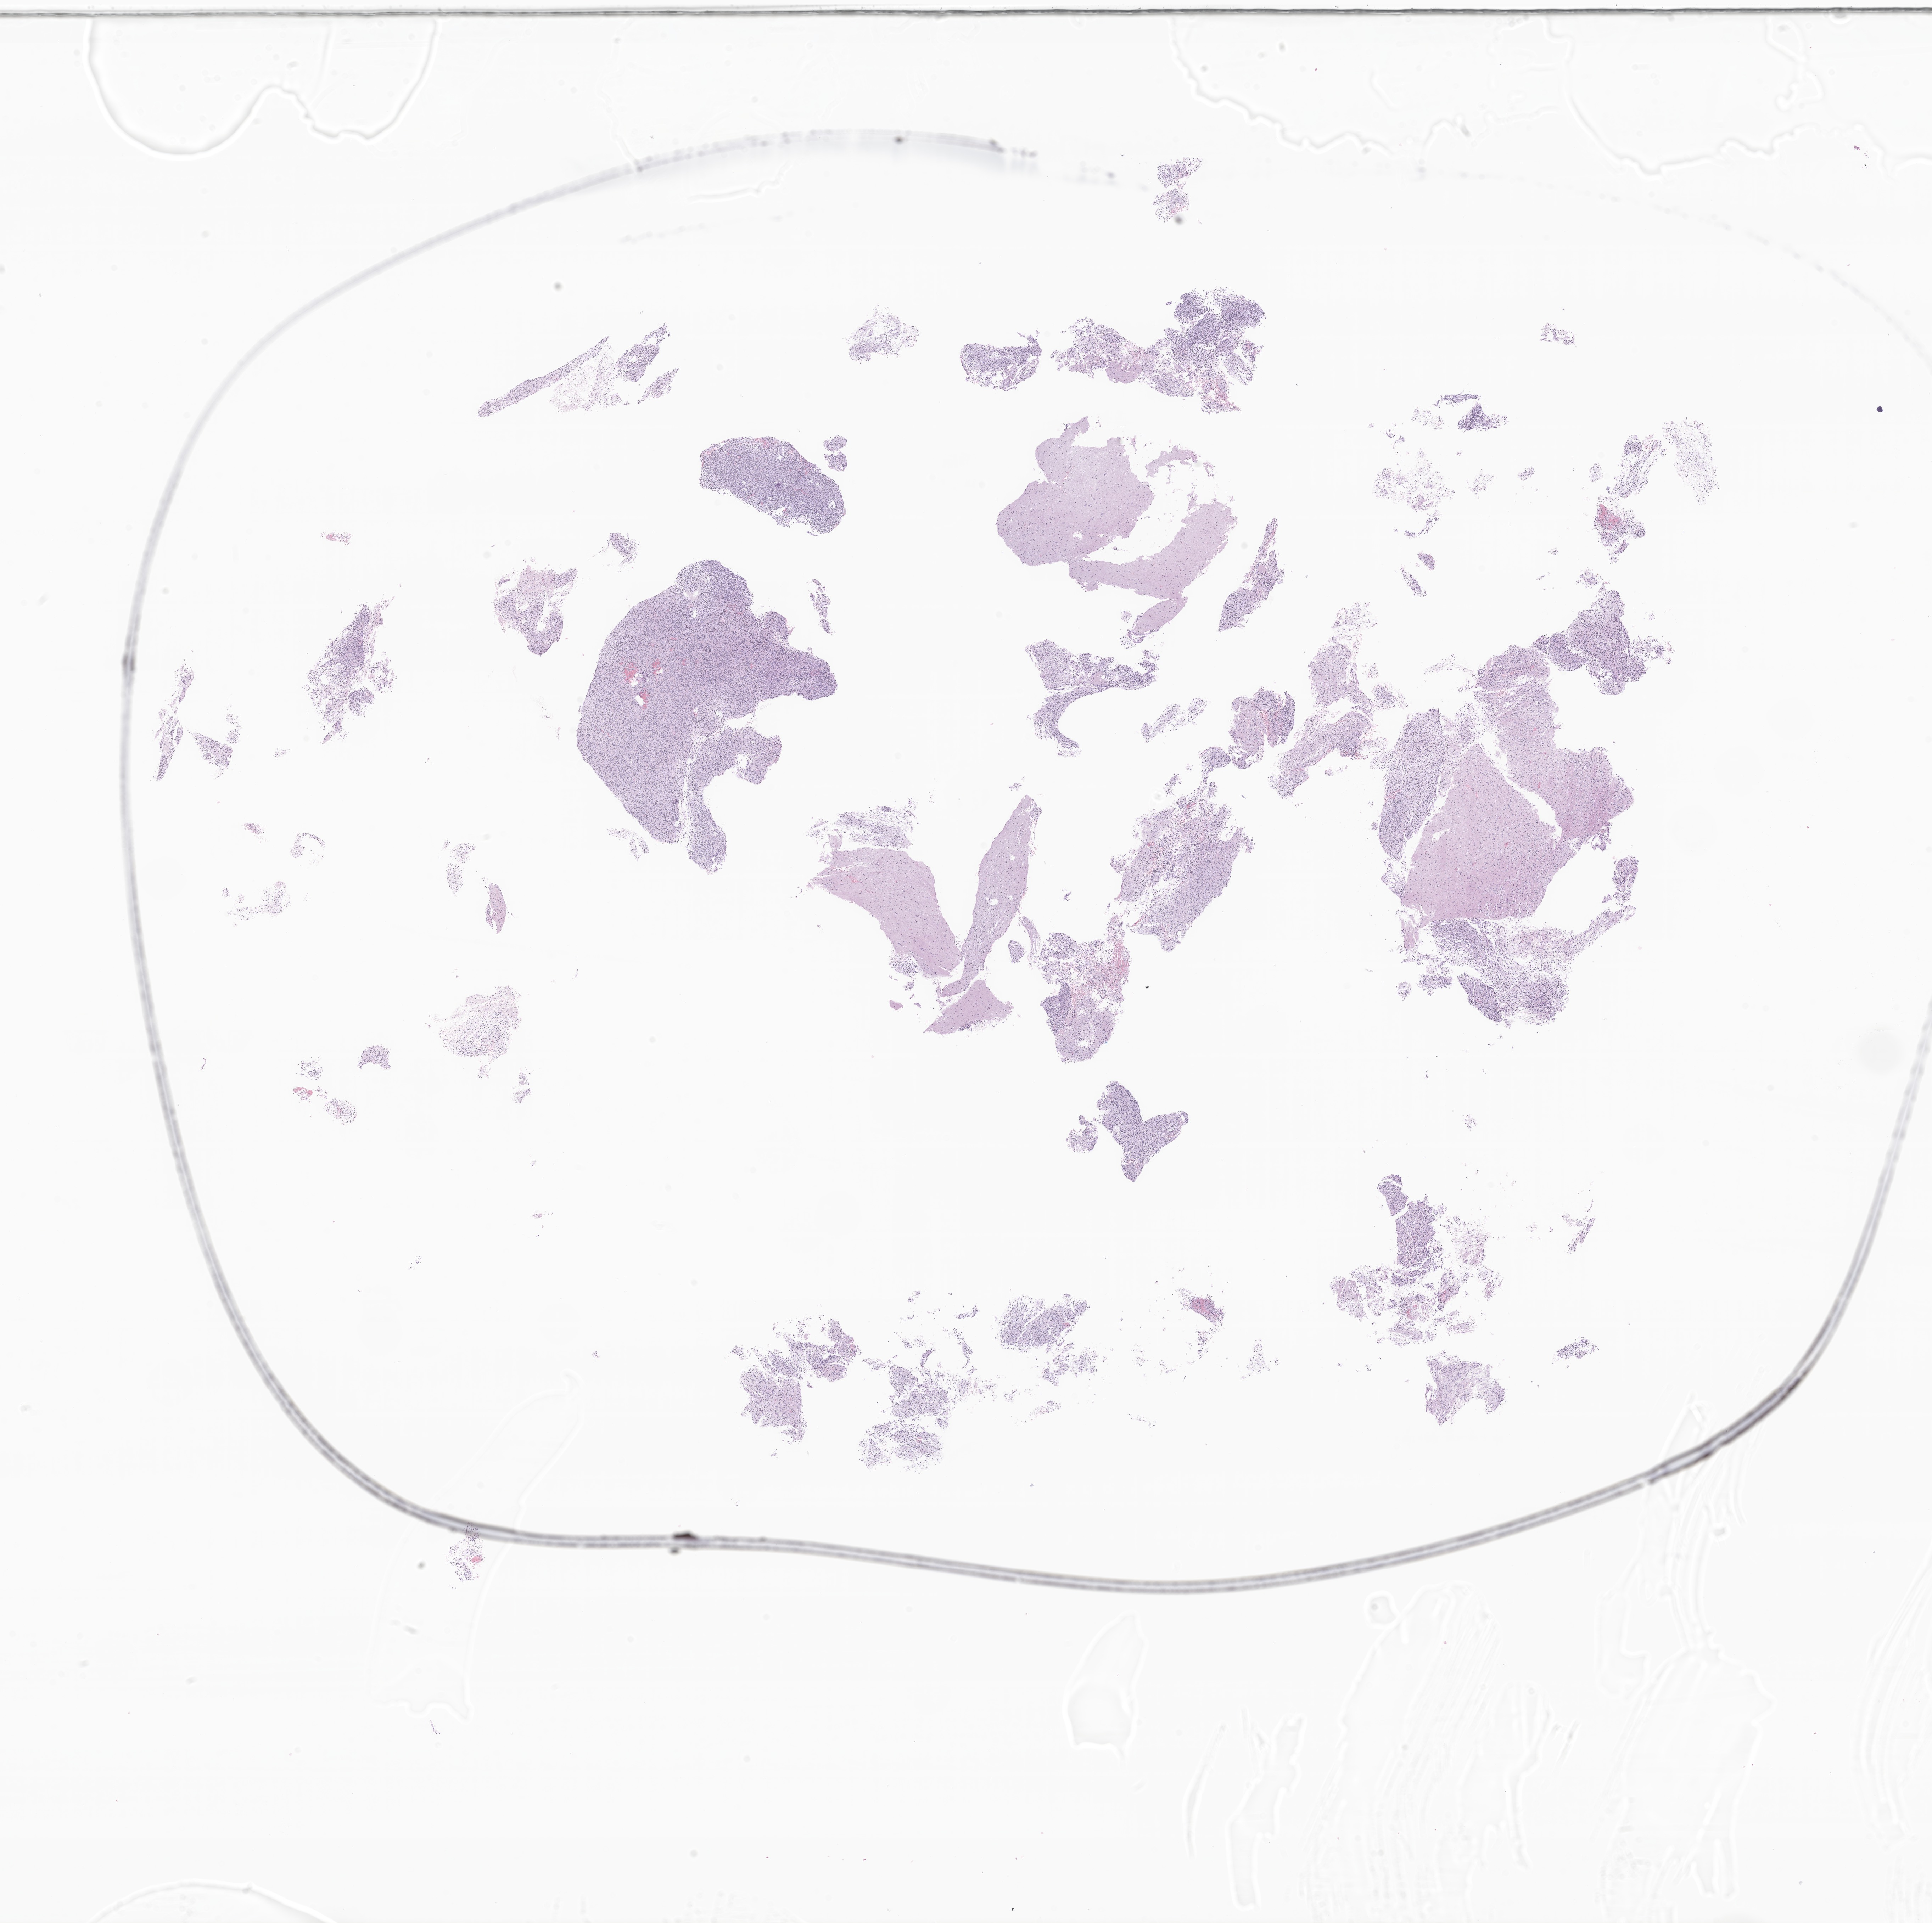
Whole-slide image, hematoxylin and eosin (H&E) stain of tumor tissue from the brain, whole scanned area (about 23.0 x 22.9 mm) shown as a low-resolution overview; formalin-fixed, paraffin-embedded (FFPE) tissue. Male patient, age 160 months.
Diagnosis: Glioma, malignant.